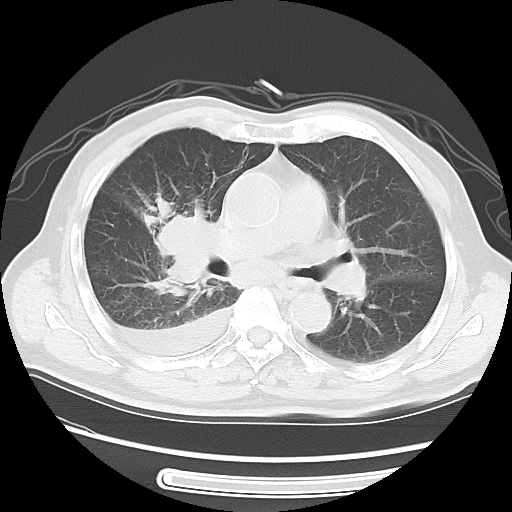
Chest CT, one axial slice; slice 31 of 56 in the series (ordered by position); reconstruction kernel LUNG; 120 kVp; lung window (W 1500 / L -600 HU); 5 mm slice thickness; 512 × 512 image matrix, field of view 360 × 360 mm. Male patient, age 77 years. From the clinical record (not read from this slice): clinical TNM (as recorded): T3 N3 M1b.
Outlined on this slice (bounding box drawn by a radiologist):
- lung tumour (recorded histology: small cell carcinoma): bounding box [x1, y1, x2, y2] px = [148, 205, 233, 292]